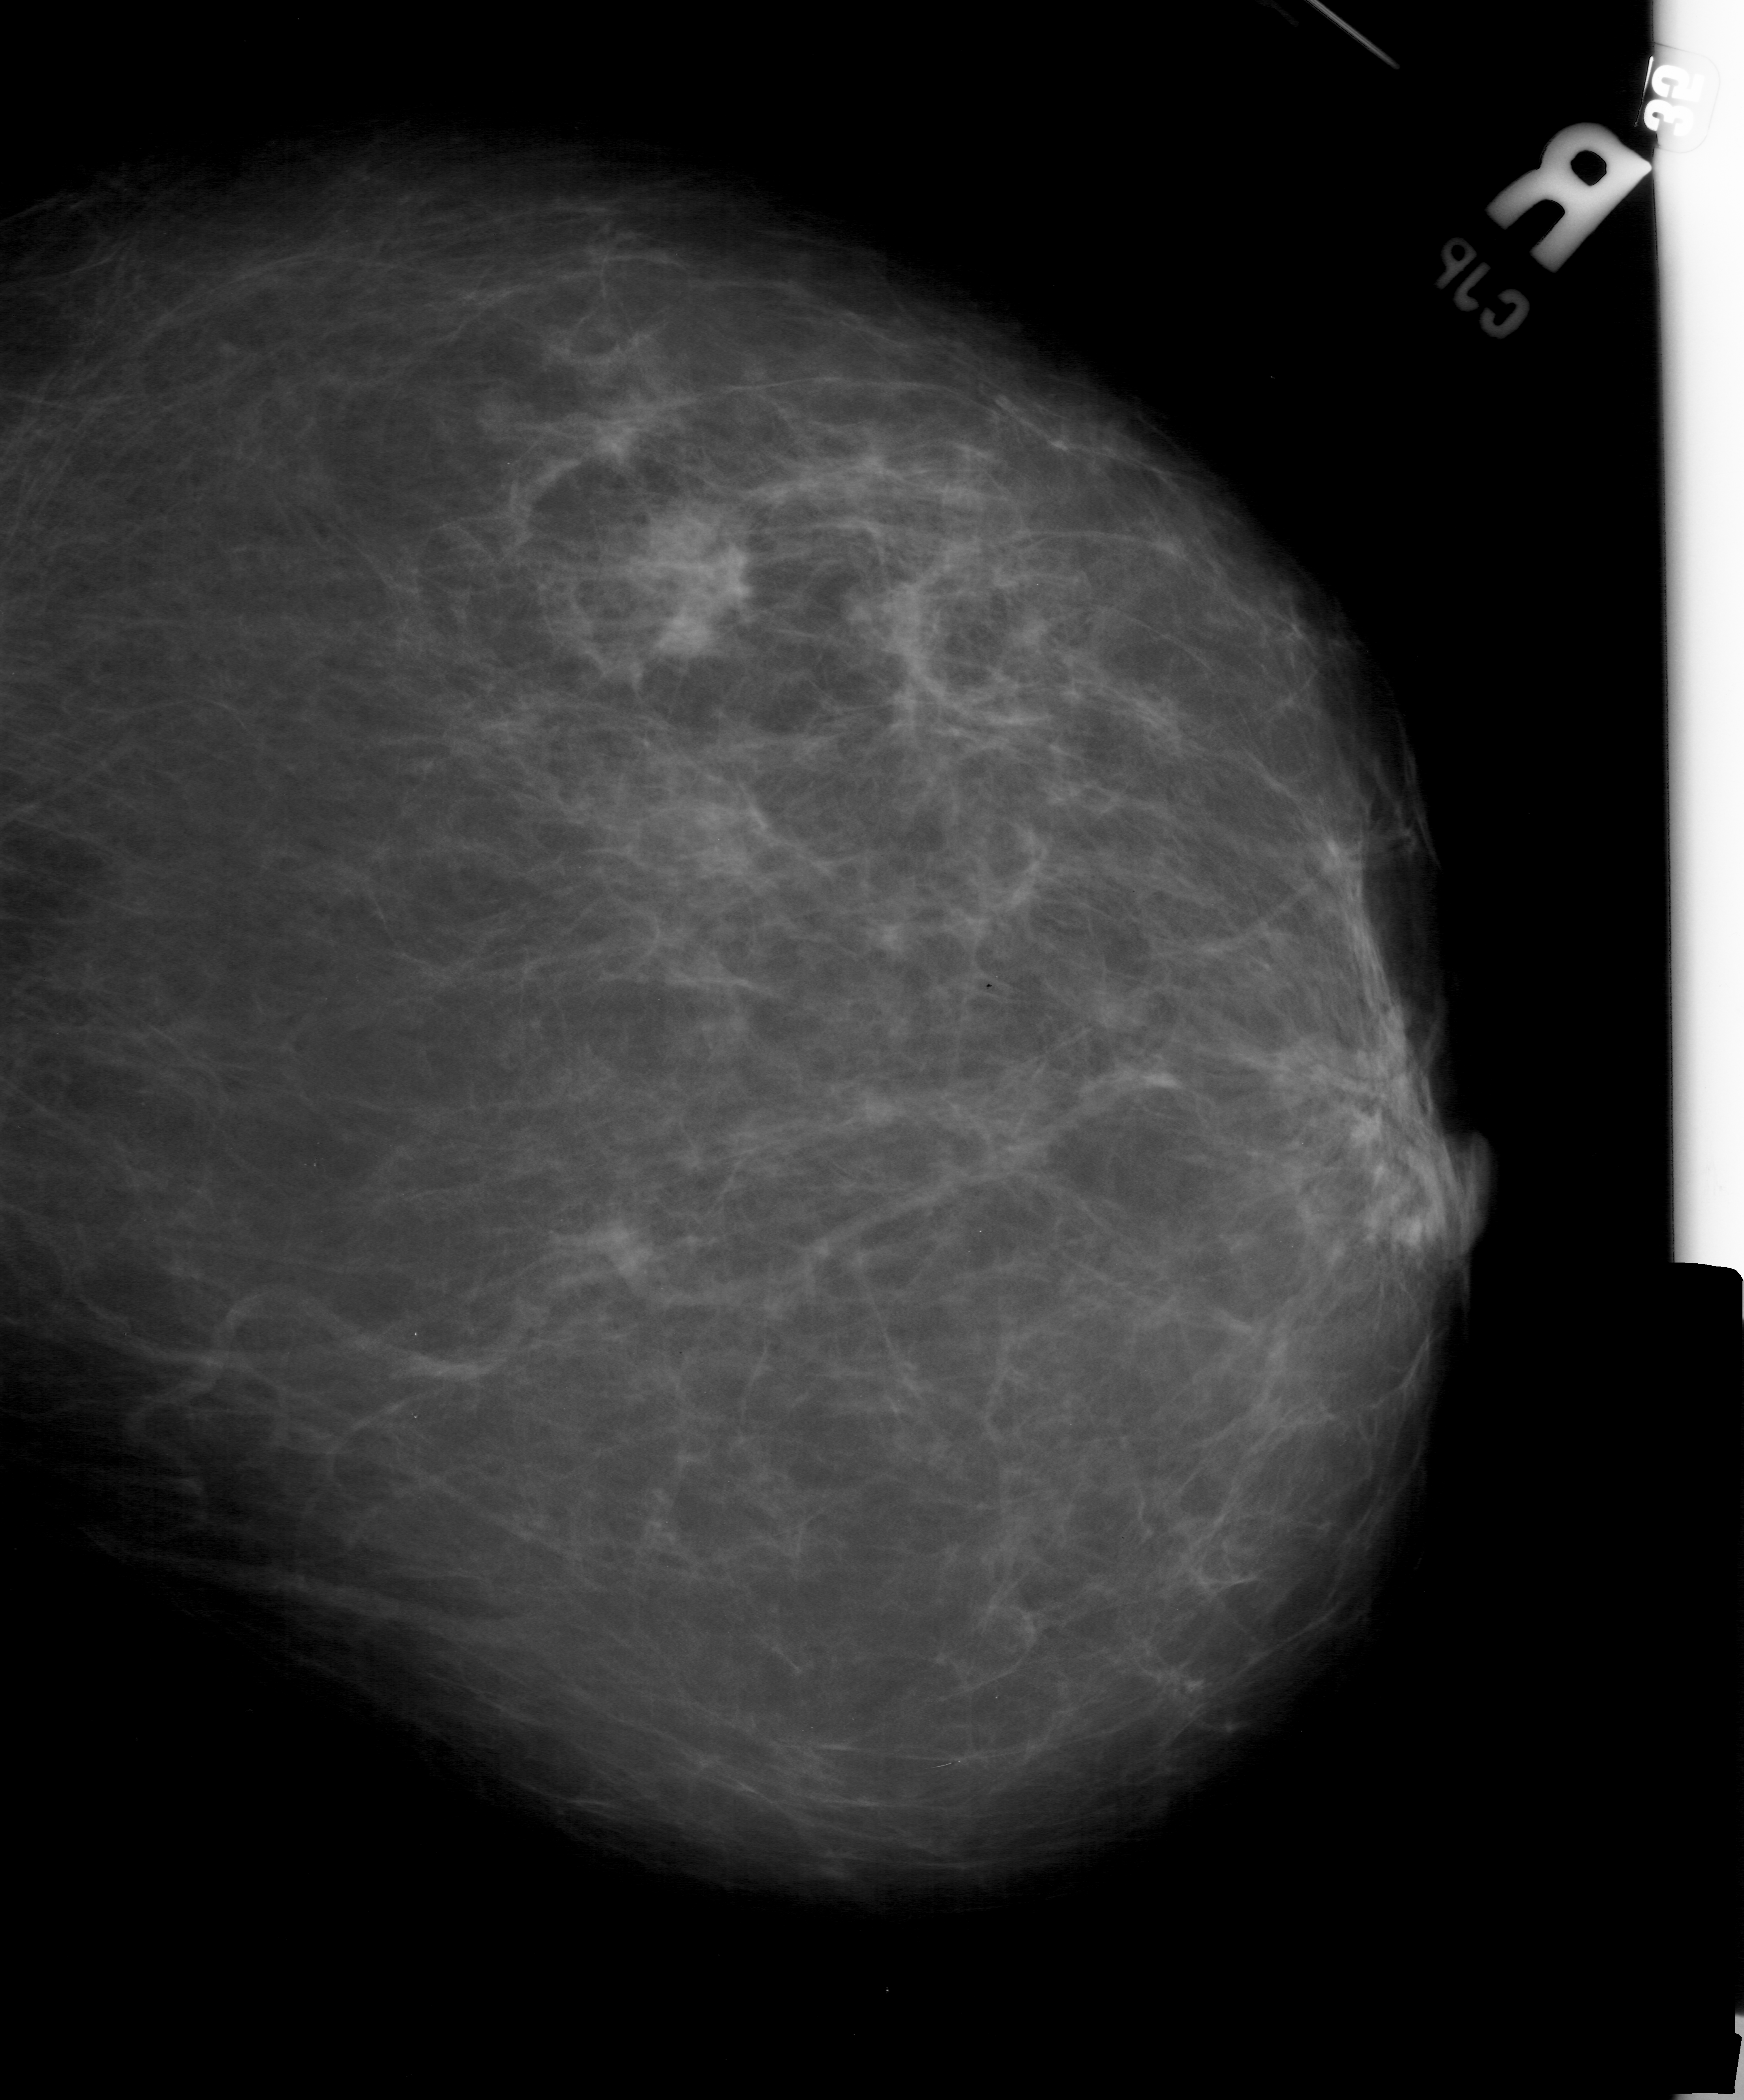
Scanned film-screen mammogram. Right breast. Craniocaudal (CC) view. 1744 × 2100 image matrix.
Expert-marked regions of interest on this film, with their recorded descriptors:
- mass, shape irregular, margins ill defined; BI-RADS assessment category 4; subtlety rating 4 on a 1 (subtle) to 5 (obvious) scale; pathology result (as recorded, not read from the image): malignant: bounding box <610,491,757,659> (left, top, right, bottom; pixels)